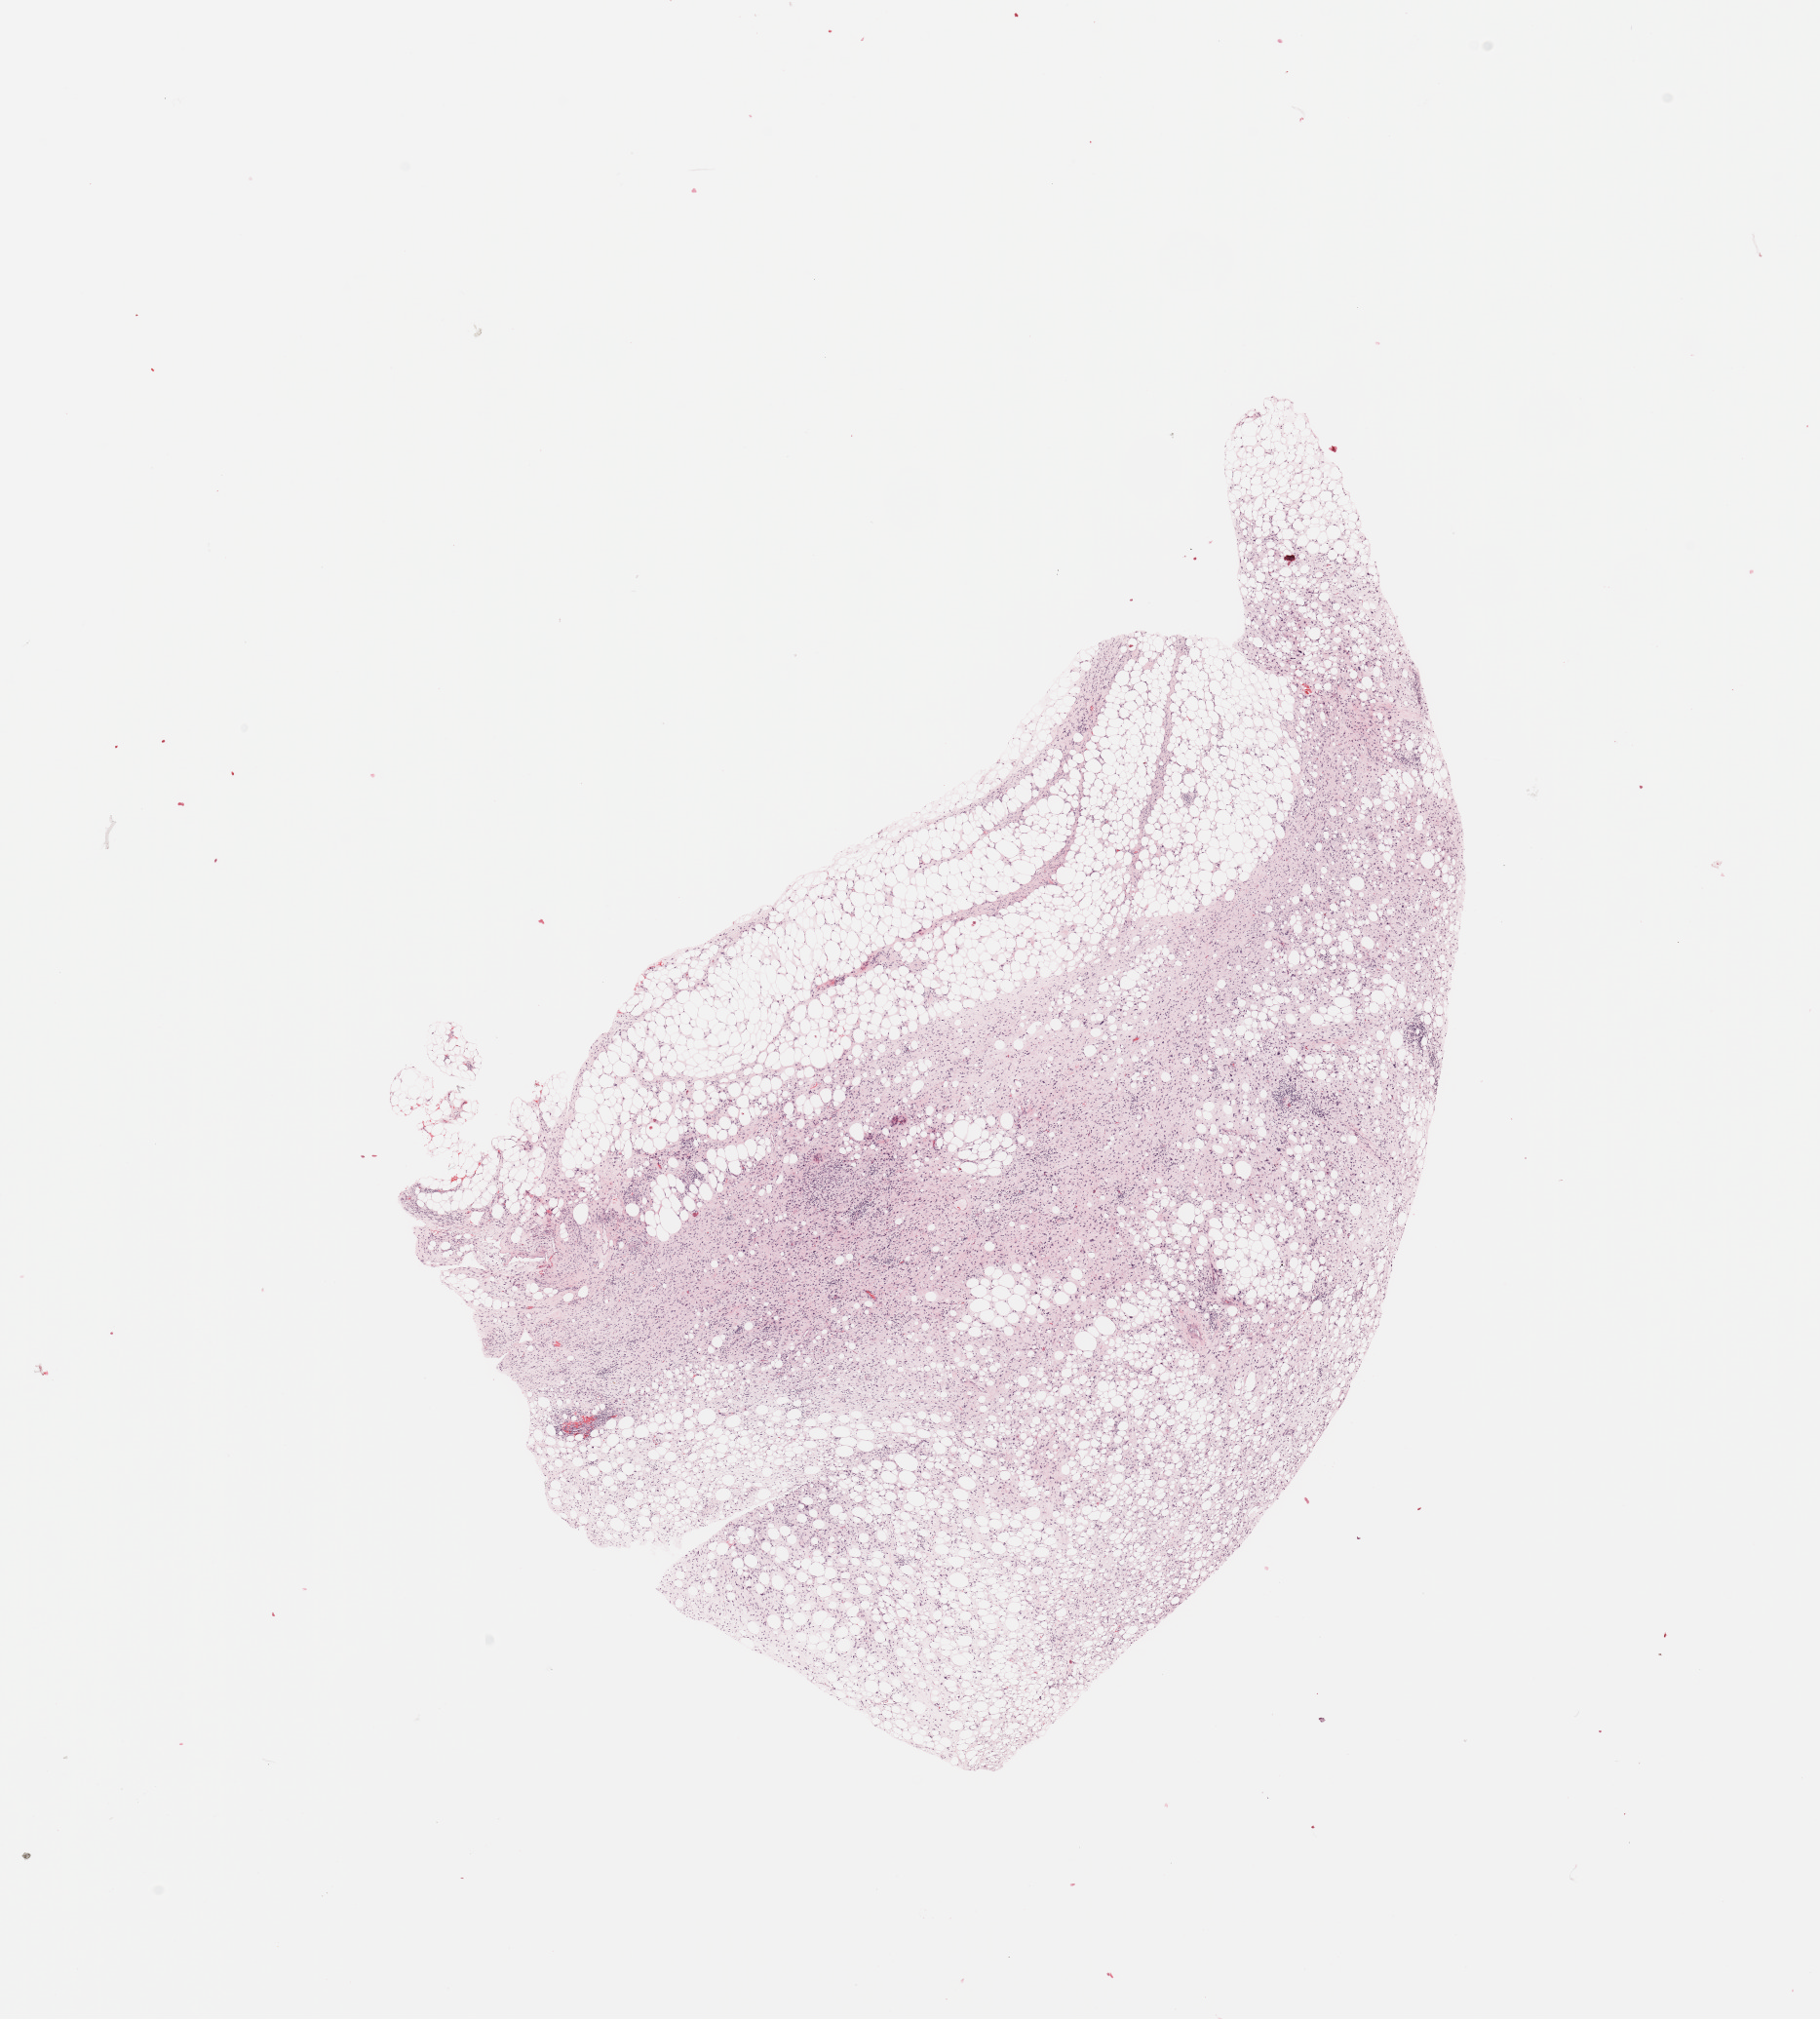
Digitized H&E tissue section (whole slide) — whole scanned area (about 14.8 x 16.4 mm, from a 20x scan) shown as a low-resolution overview, tumour tissue sample. Patient: male, age 64 years.
Patient diagnosis (cohort enrolment): sarcoma (site not recorded at cohort level).